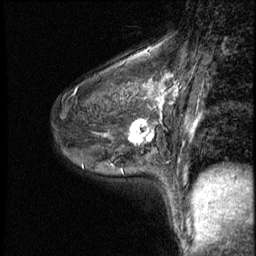
Breast MRI (dynamic contrast-enhanced), one sagittal slice. Position 36 of 50 along the scan axis. 3 images stored at this slice position (order not interpretable as contrast timing). 1.5 T. TE 4.2 ms, TR 8.7 ms. 256 × 256 image matrix, field of view 180 × 180 mm. Female patient, age 43 years. From the clinical record (not read from this slice): setting: breast cancer imaged before/during neoadjuvant chemotherapy; receptor status: HR-positive, HER2-negative.
Structures marked on this image (semi-automatically segmented with operator editing):
- analysis volume of interest (the breast-tissue region the enhancement analysis was run in; not a lesion): bounding box <122,109,159,155> (left, top, right, bottom; pixels)
- tumour enhancement mask (voxels above the 140 % enhancement threshold inside the analysis volume of interest): <129,119,157,144>